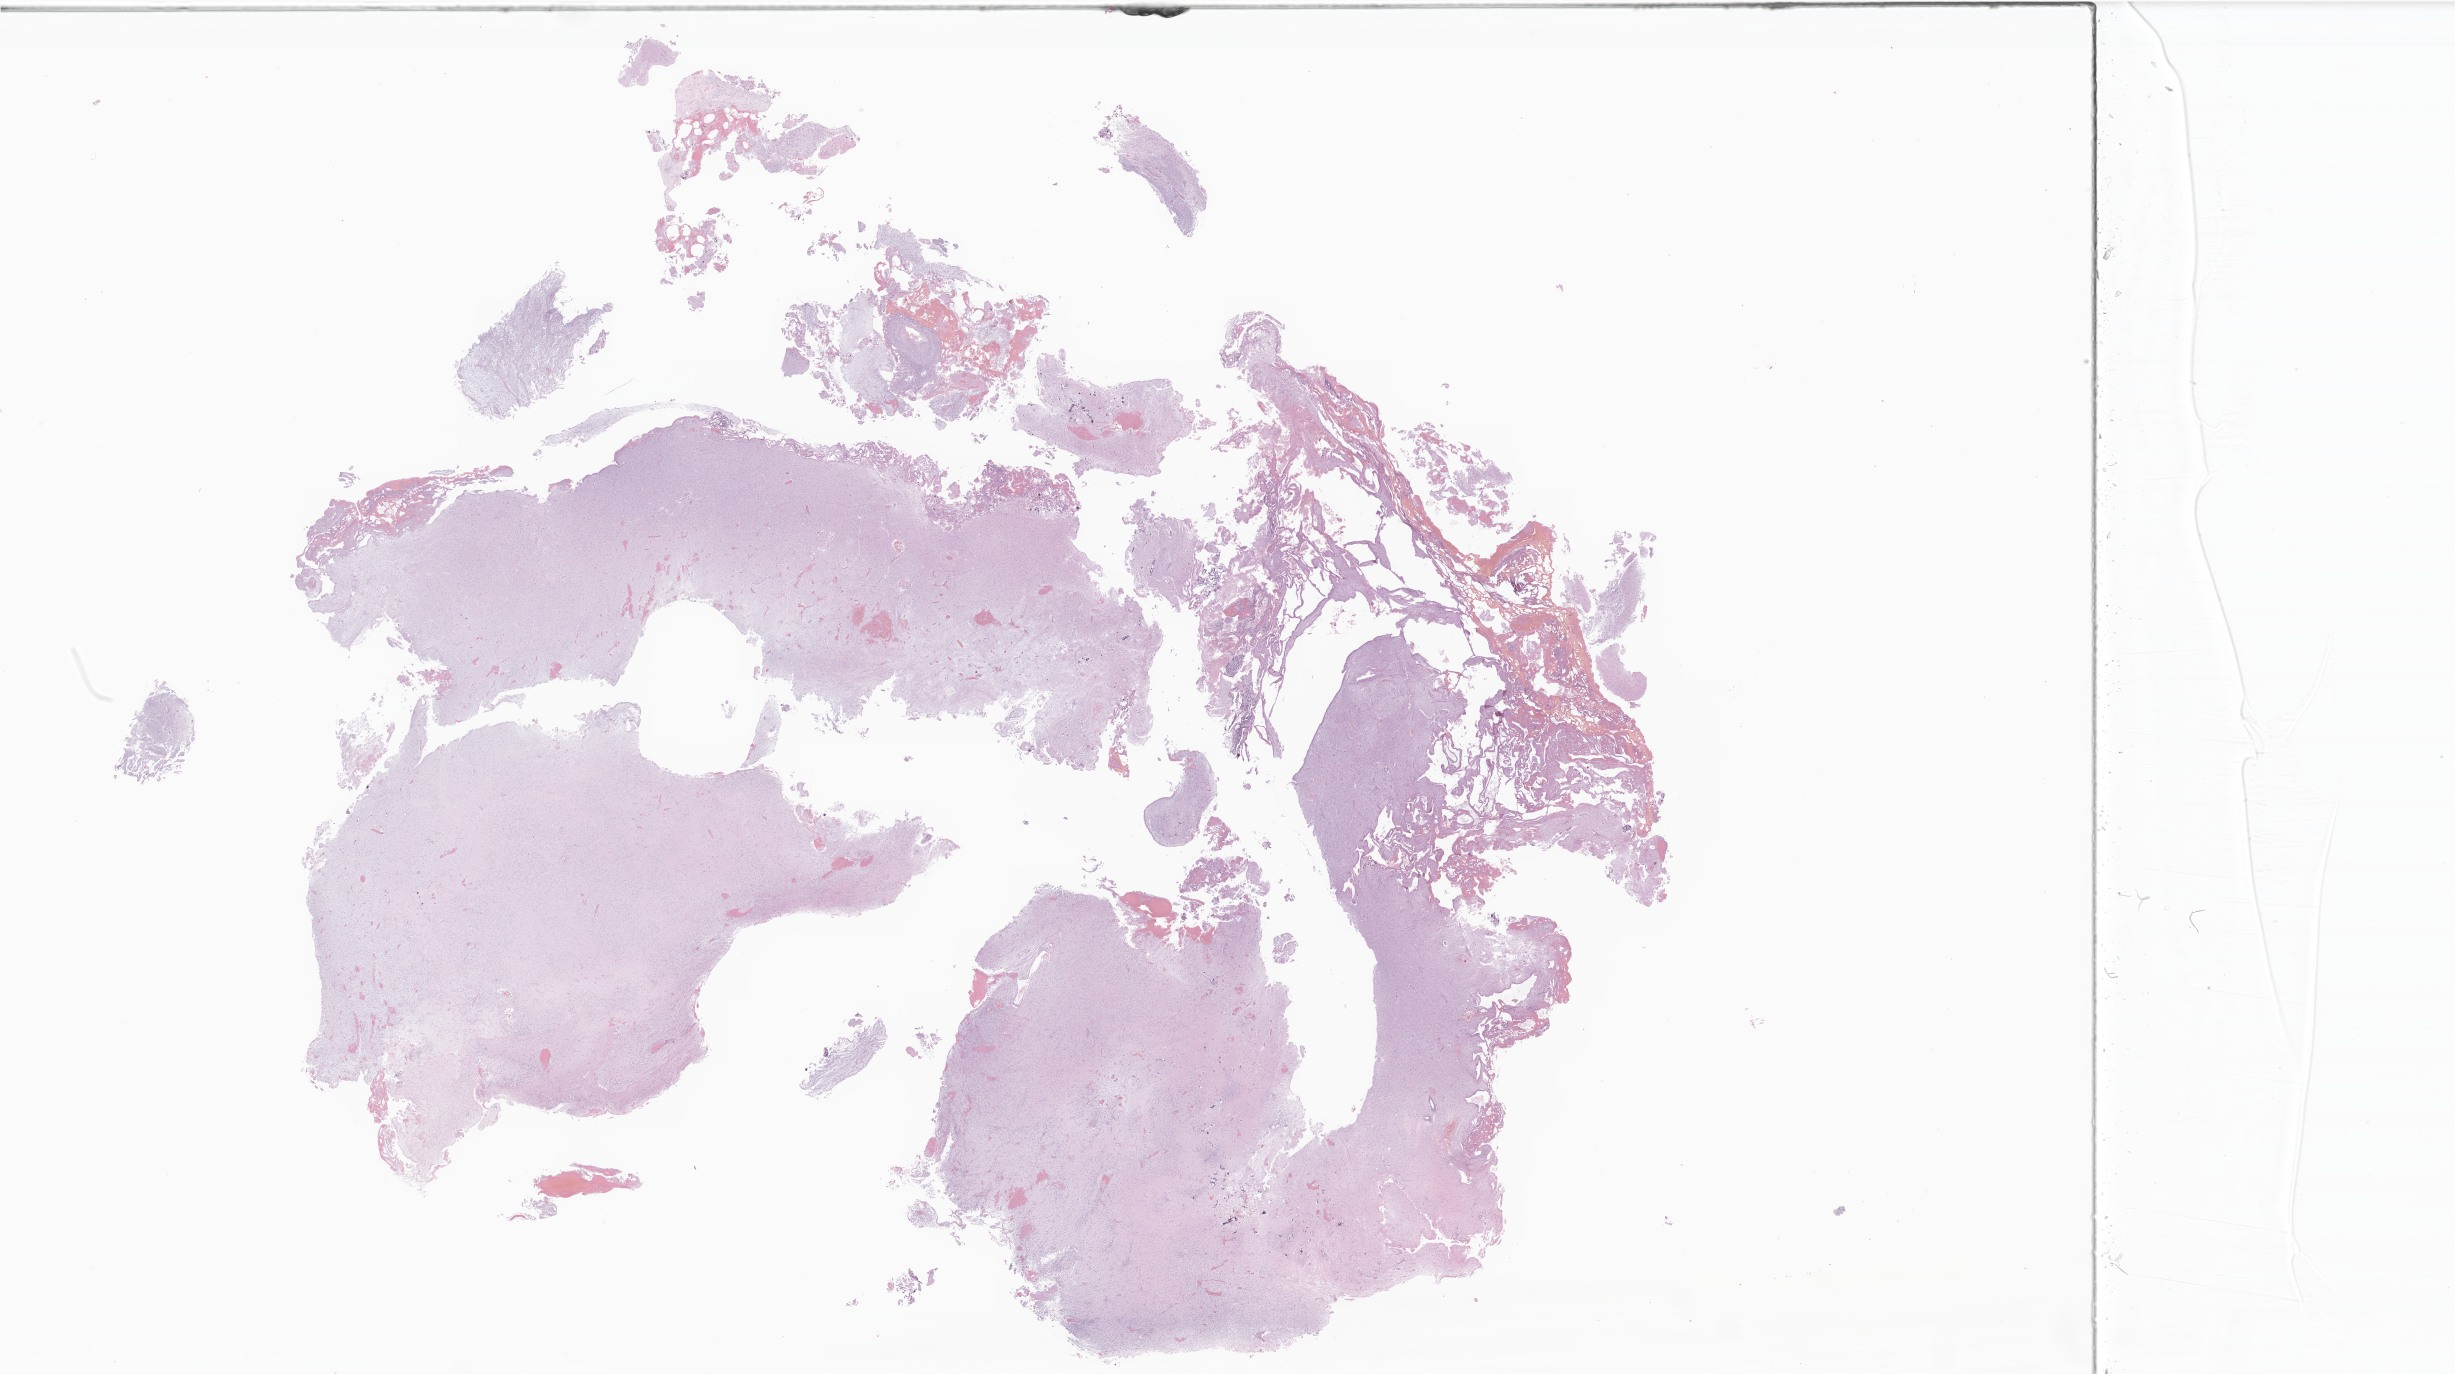
Digitized hematoxylin and eosin (H&E)-stained section of tumor tissue from the cerebral ventricle, whole scanned area (about 41.4 x 23.2 mm) shown as a low-resolution overview; formalin-fixed, paraffin-embedded (FFPE) tissue. Patient male; age 117 months (9 years 9 months).
- recorded diagnosis: Pilocytic astrocytoma